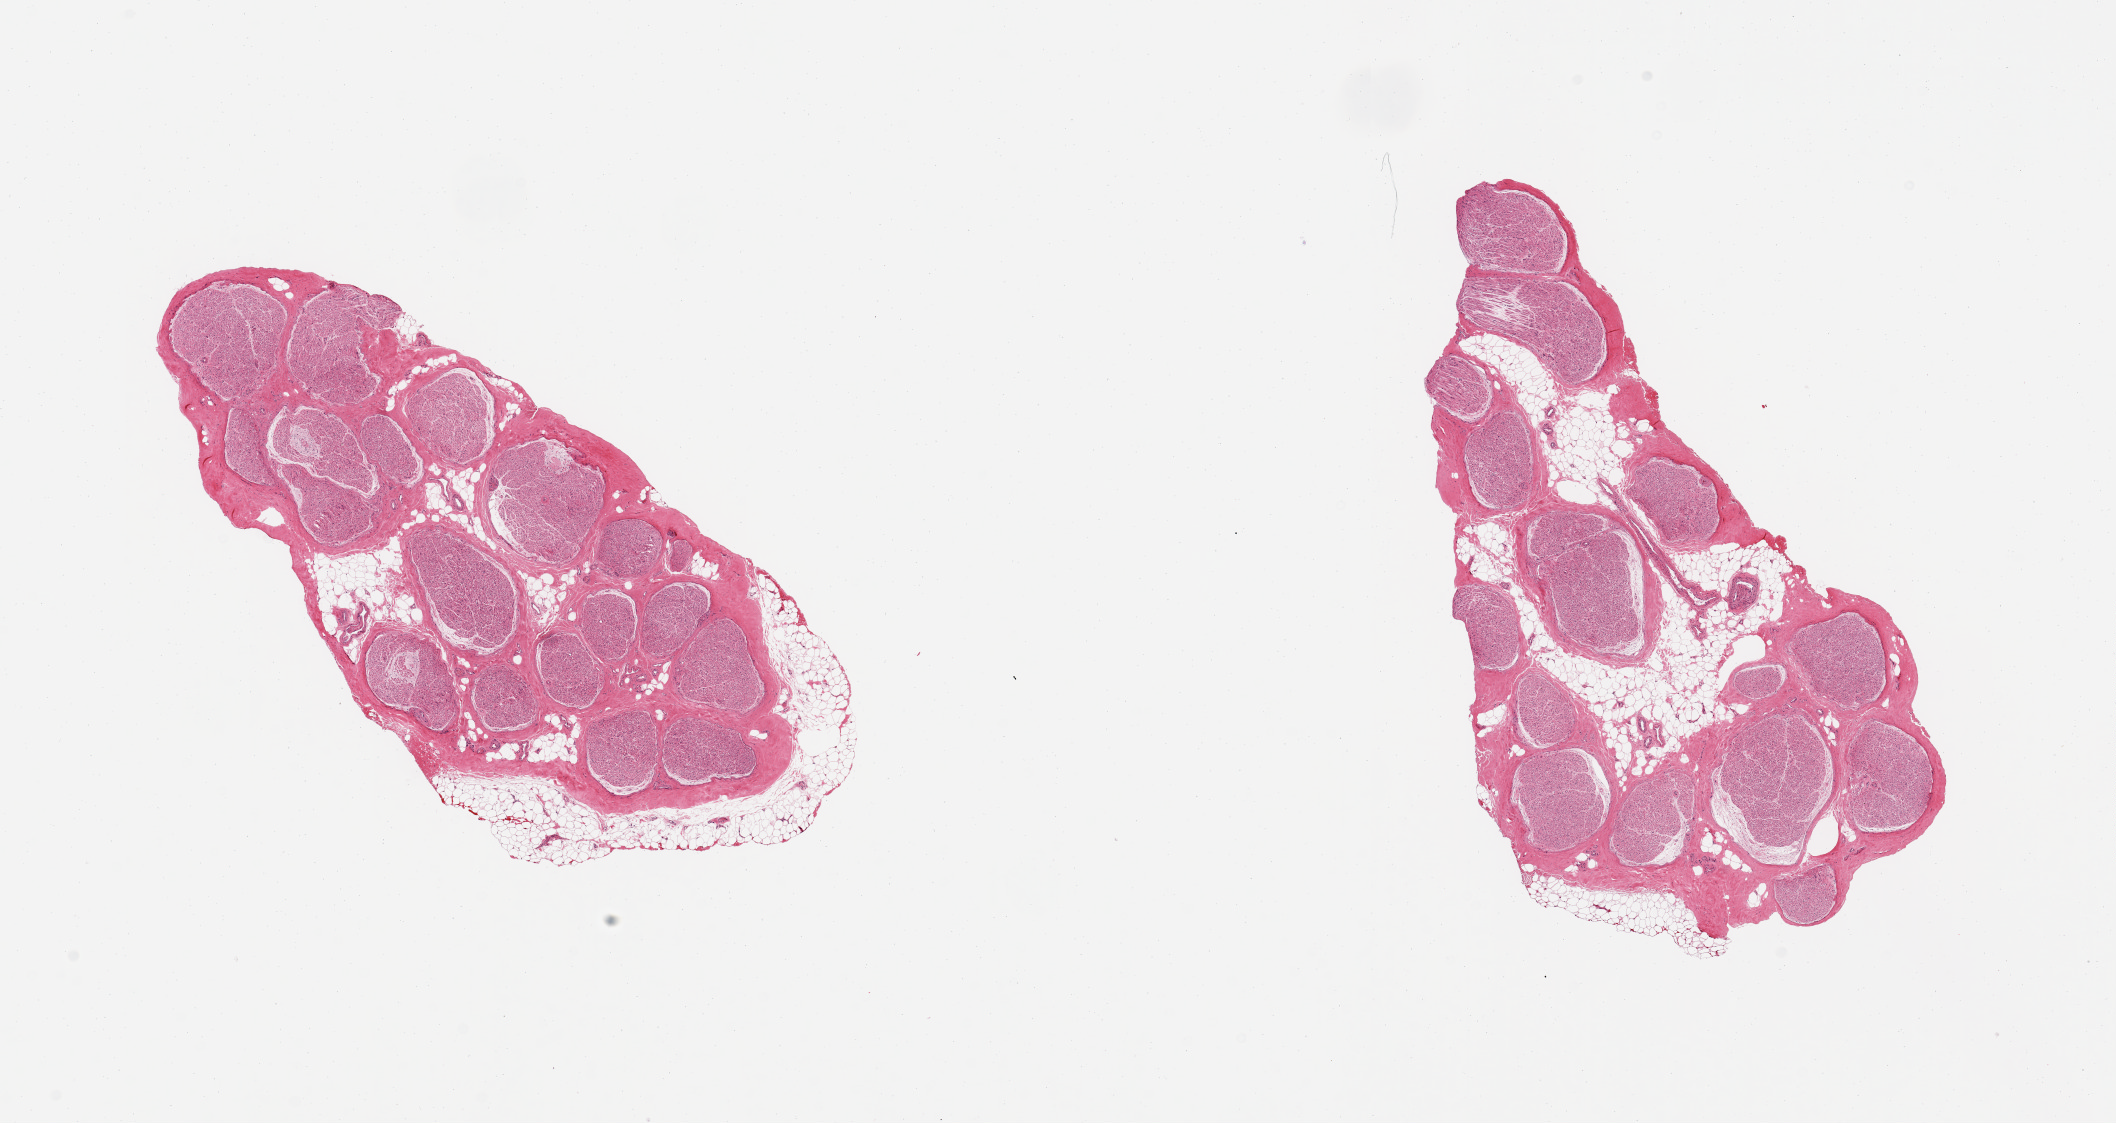
Hematoxylin and eosin (H&E) whole-slide image, brightfield — shown as a low-resolution overview of the whole scanned area (about 16.7 x 8.9 mm, slide scanned at 20x). PAXgene-fixed paraffin-embedded (PFPE) section. Target tissue: tibial nerve. Tissue donor sample. Donor: male.
• review note (as recorded): 2 pieces; adherent fat up to 0.6mm and ~ 5 - 10% internal fat